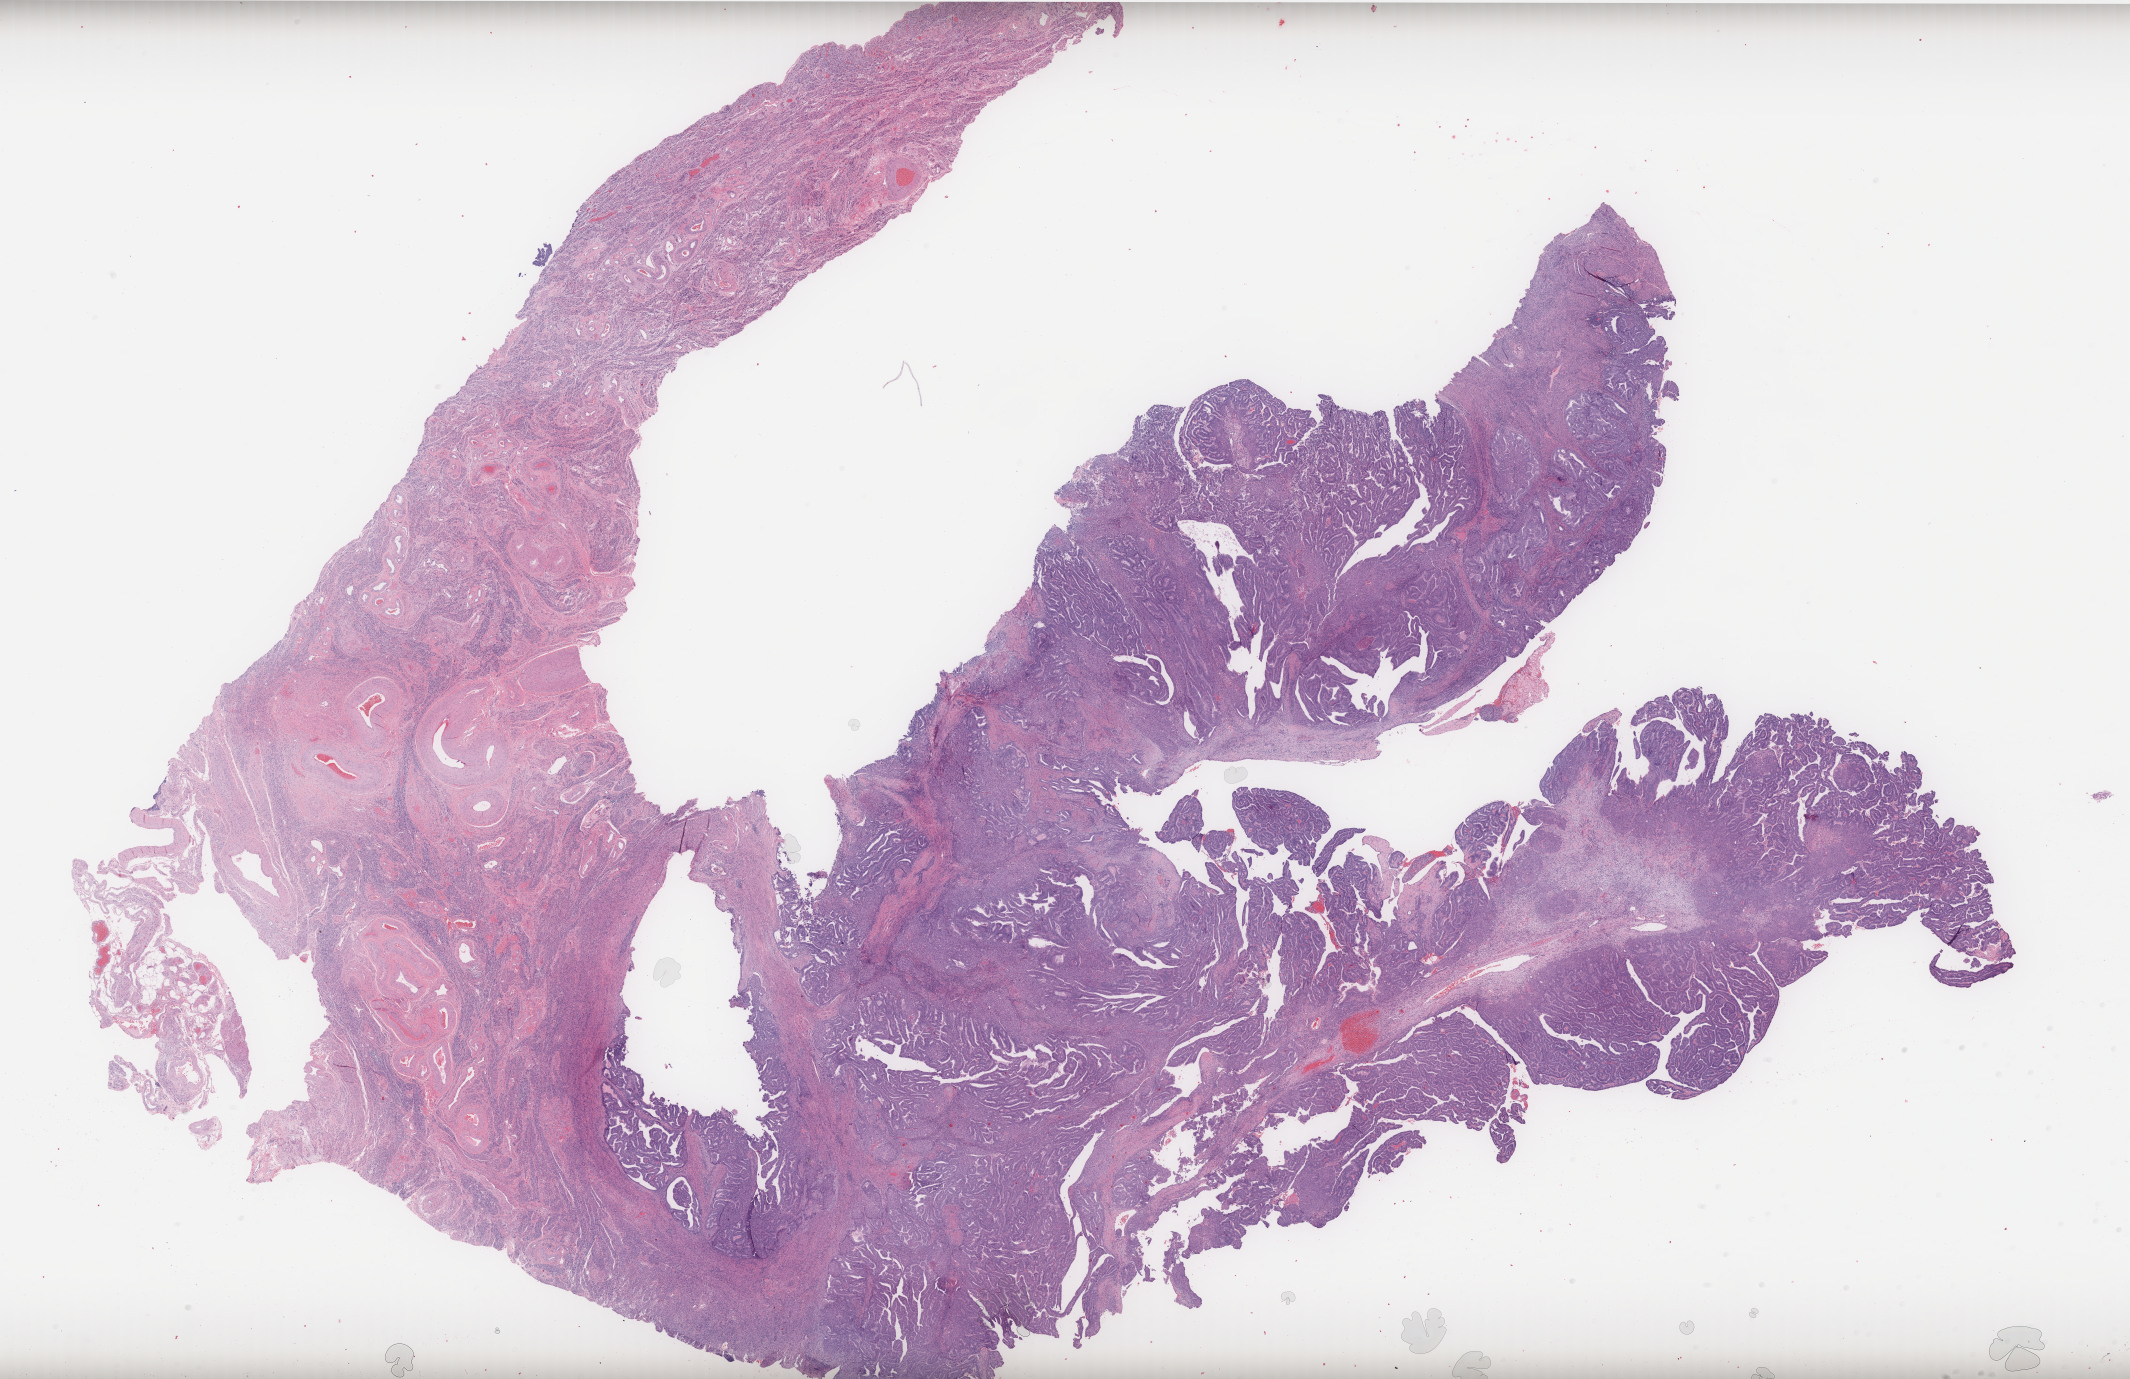
Hematoxylin and eosin (H&E) stained whole-slide image, whole scanned area (about 34.2 x 22.1 mm, acquisition: 40x scan) shown as a low-resolution overview. FFPE section. Uterus, primary tumour sample. Patient: female, age at initial diagnosis 63 years. Histologic grade: G1 (well differentiated).
Diagnosis: Endometrioid adenocarcinoma, NOS (endometrium). FIGO stage: IA.